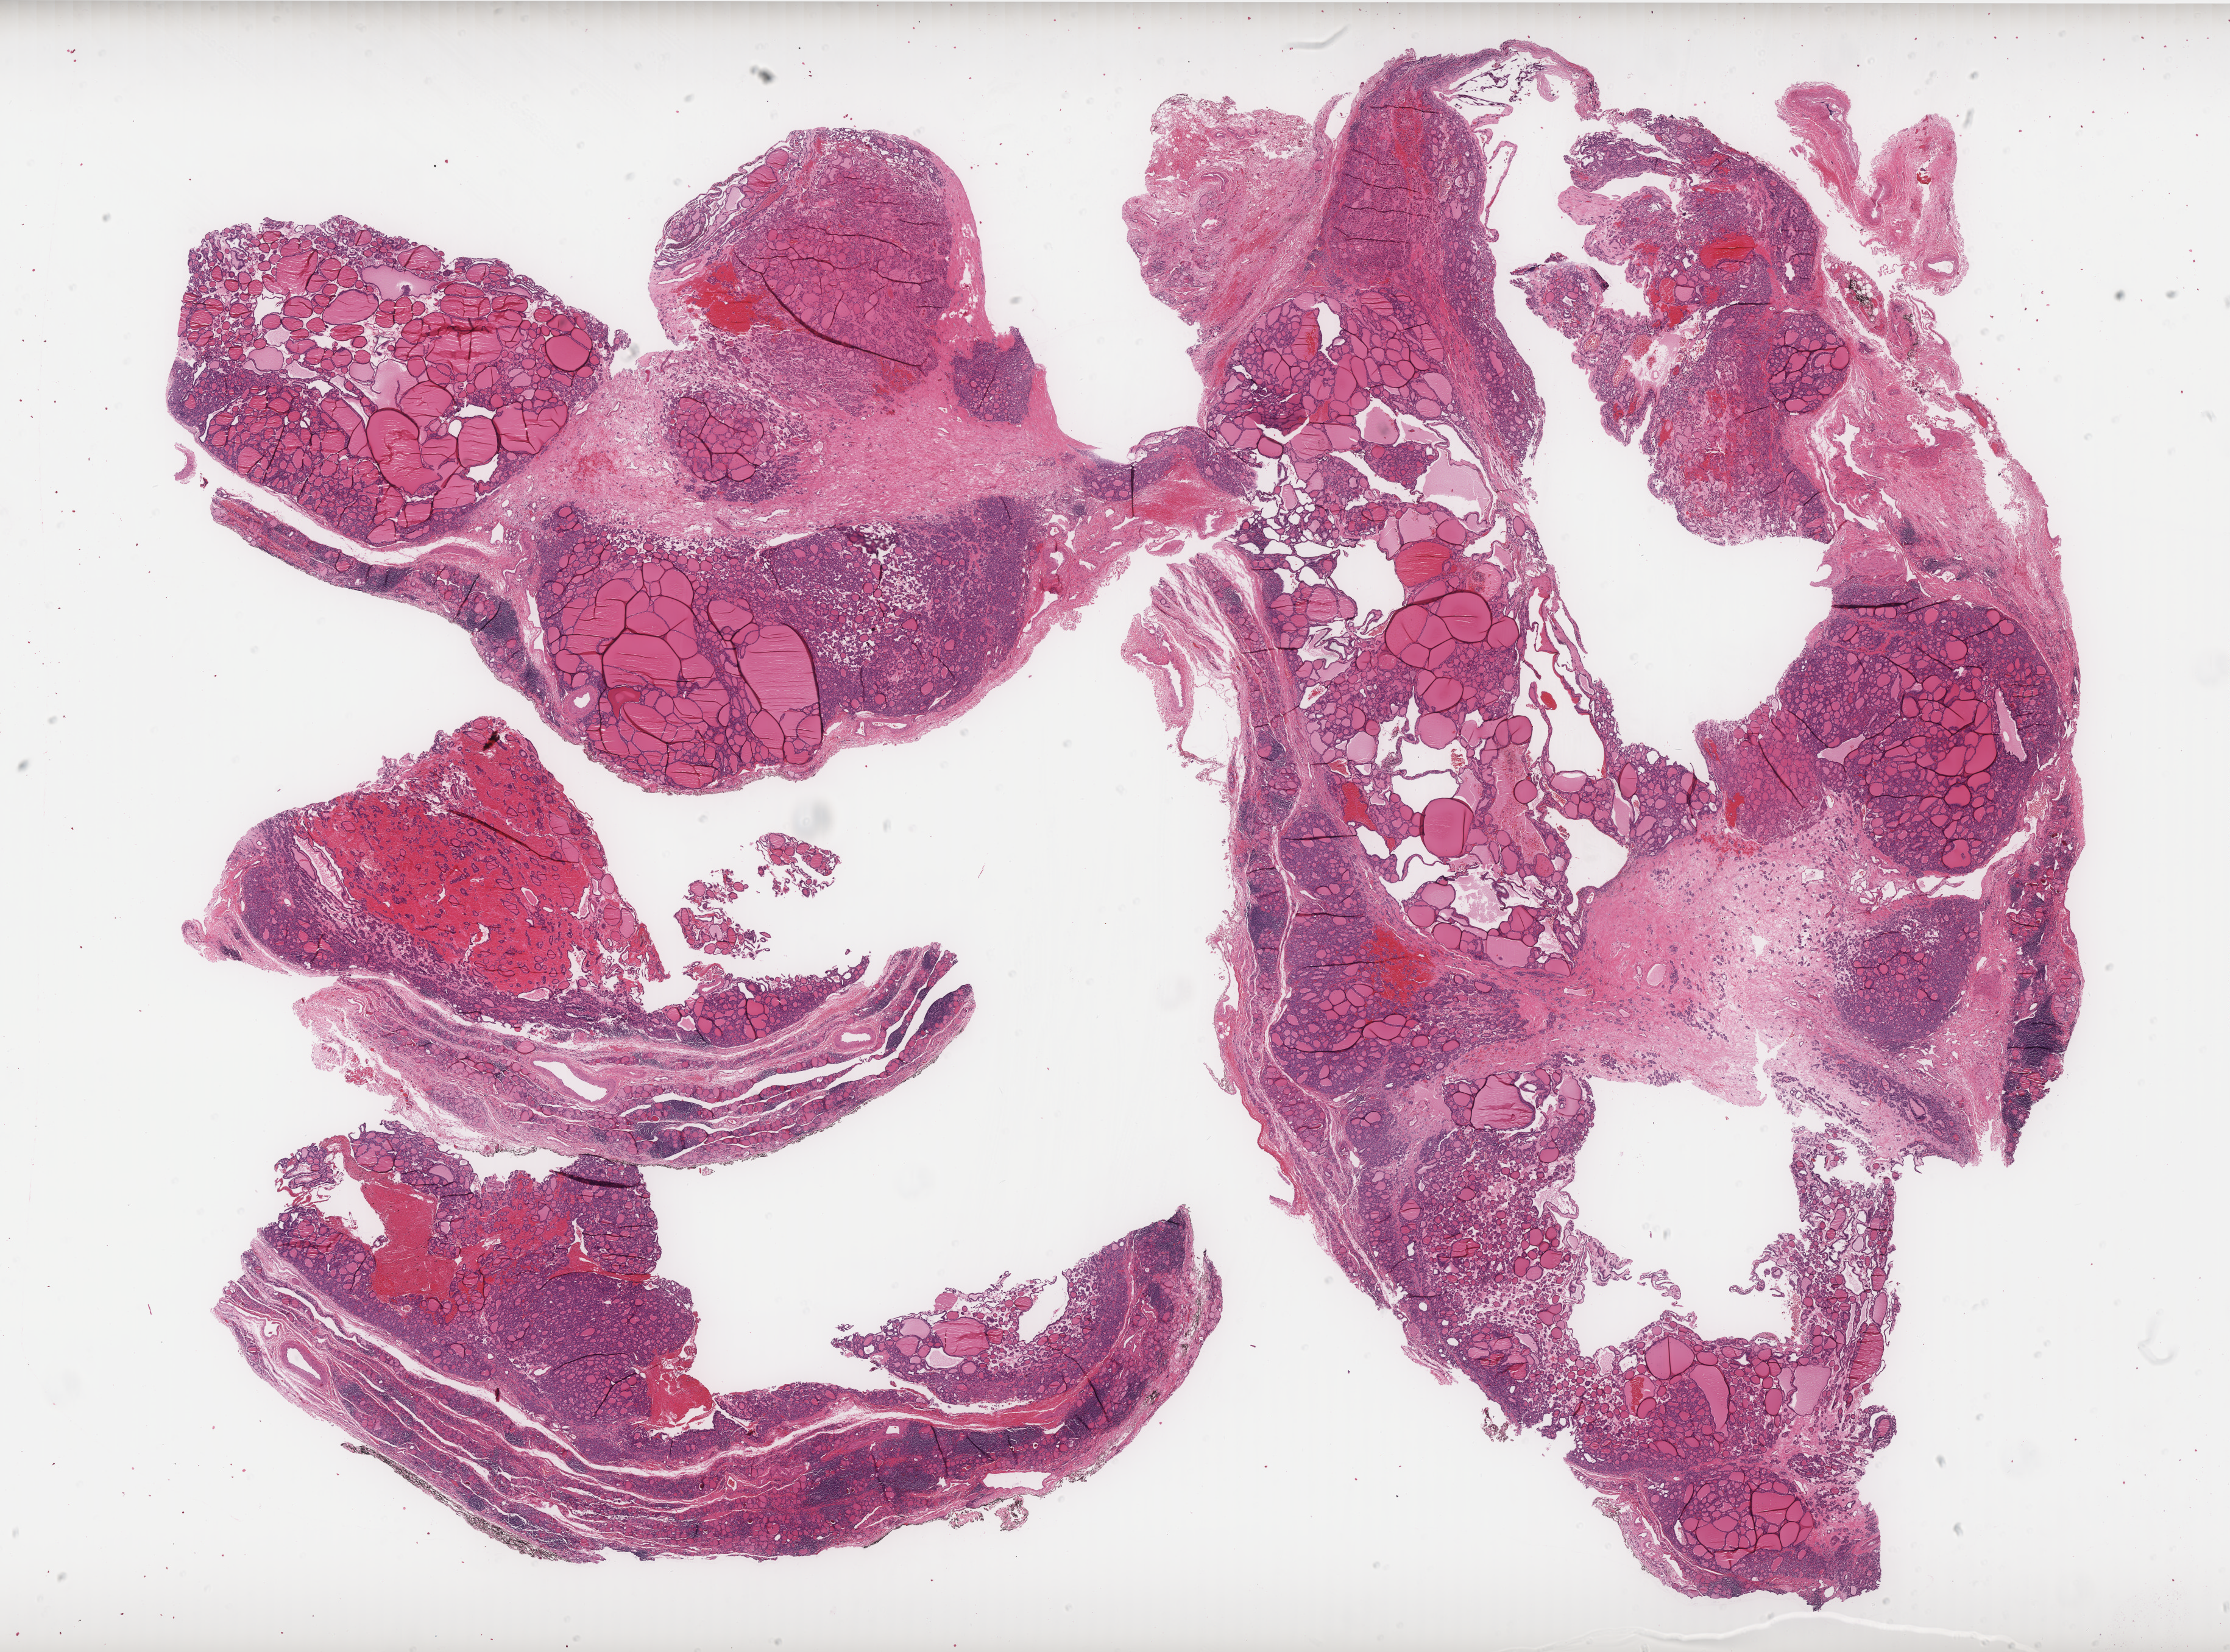
Whole-slide histology image, Hematoxylin and eosin (H&E) stained, a low-resolution overview of the entire scanned area, about 29.3 x 21.7 mm, formalin-fixed paraffin-embedded (FFPE) diagnostic section, primary tumour sample from the thyroid. Female patient; age at initial diagnosis 67 years.
• TNM: T2 N0 M0
• diagnosis: Papillary adenocarcinoma, NOS (thyroid gland)
• laterality: bilateral
• AJCC pathologic stage: II (7th edition)